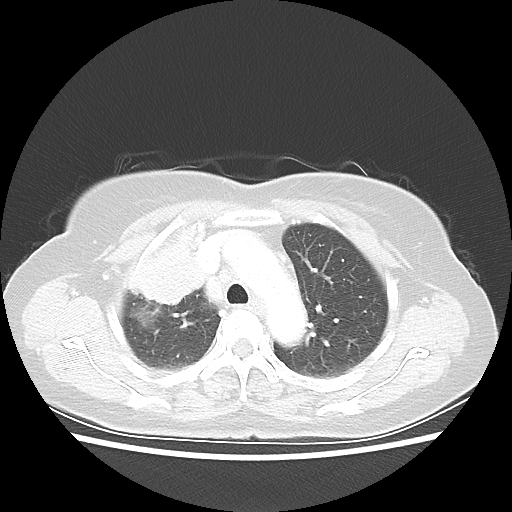
Chest CT, one axial slice. Slice 40 of 55 in the series (ordered by position). Reconstruction kernel LUNG. 80 kVp. Lung window (W 1500 / L -600 HU). 512 × 512 image matrix, field of view 337 × 337 mm. Female patient, age 62 years. From the clinical record (not read from this slice): clinical TNM (as recorded): T4 N3 M0.
Structures marked on this image (bounding box drawn by a radiologist):
- lung tumour (recorded histology: squamous cell carcinoma): bounding box (x1, y1, x2, y2) in pixels: (128, 217, 217, 312)